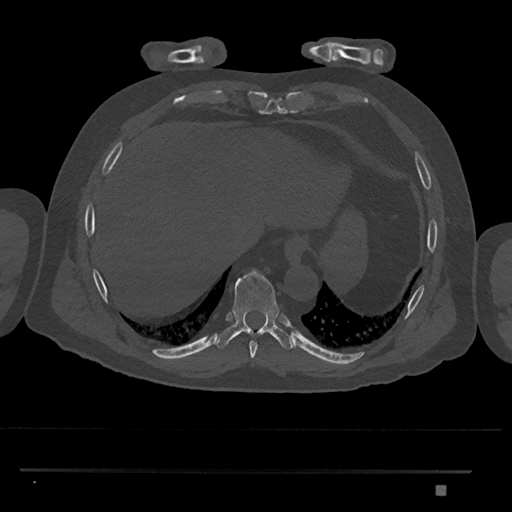
CT including the spine, one axial slice; slice 1071 of 1134 in the series (ordered by position); 120 kVp; bone window (W 1800 / L 400 HU); 512 × 512 image matrix. Male patient, age 65 years. Case-level facts recorded for this patient, not image findings: primary cancer: prostate.
Structures marked on this image (semi-automatic segmentation, software-assisted and operator-edited):
- T8 vertebra: bounding box [x1, y1, x2, y2] px = [249, 341, 258, 359]
- T9 vertebra: [215, 269, 294, 350]